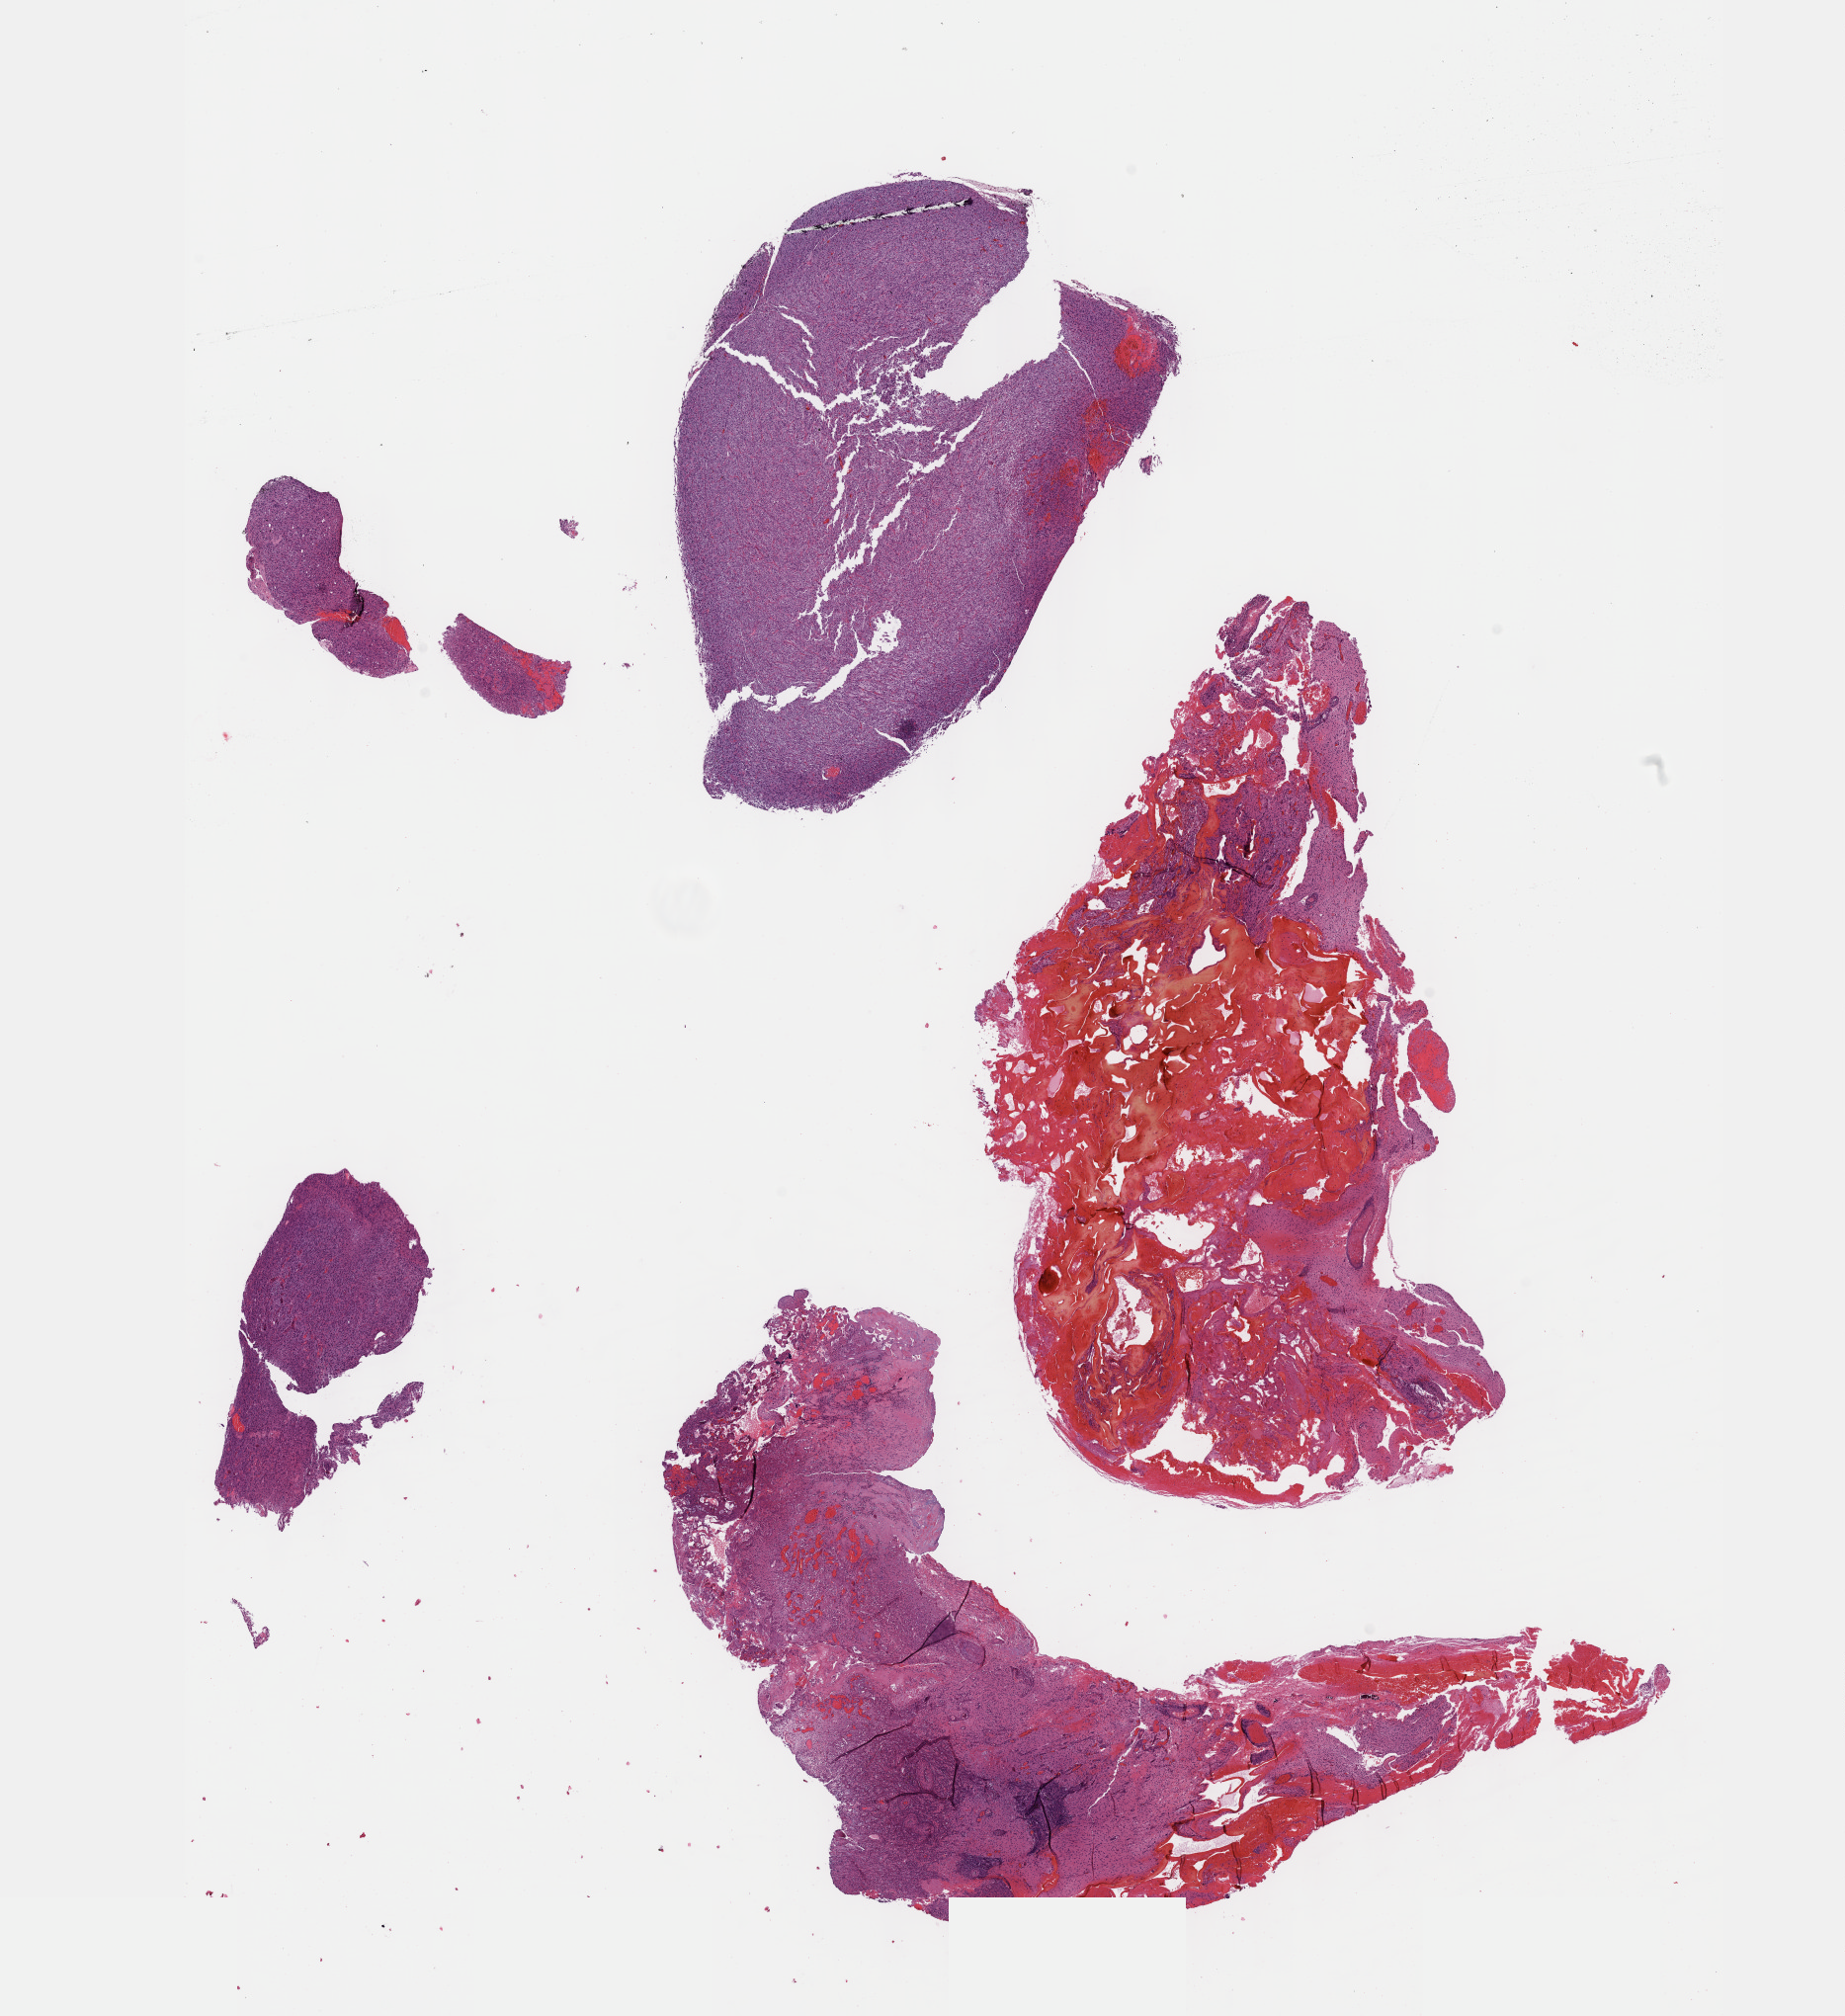
Whole-slide histology image, Hematoxylin and eosin (H&E) stained — whole scanned area (about 15.1 x 16.5 mm) shown as a low-resolution overview, FFPE section, sample: primary tumour, brain. Male, age 66 years at initial diagnosis. Histologic grade: G3 (poorly differentiated).
Diagnosis: Oligodendroglioma, anaplastic (cerebrum).